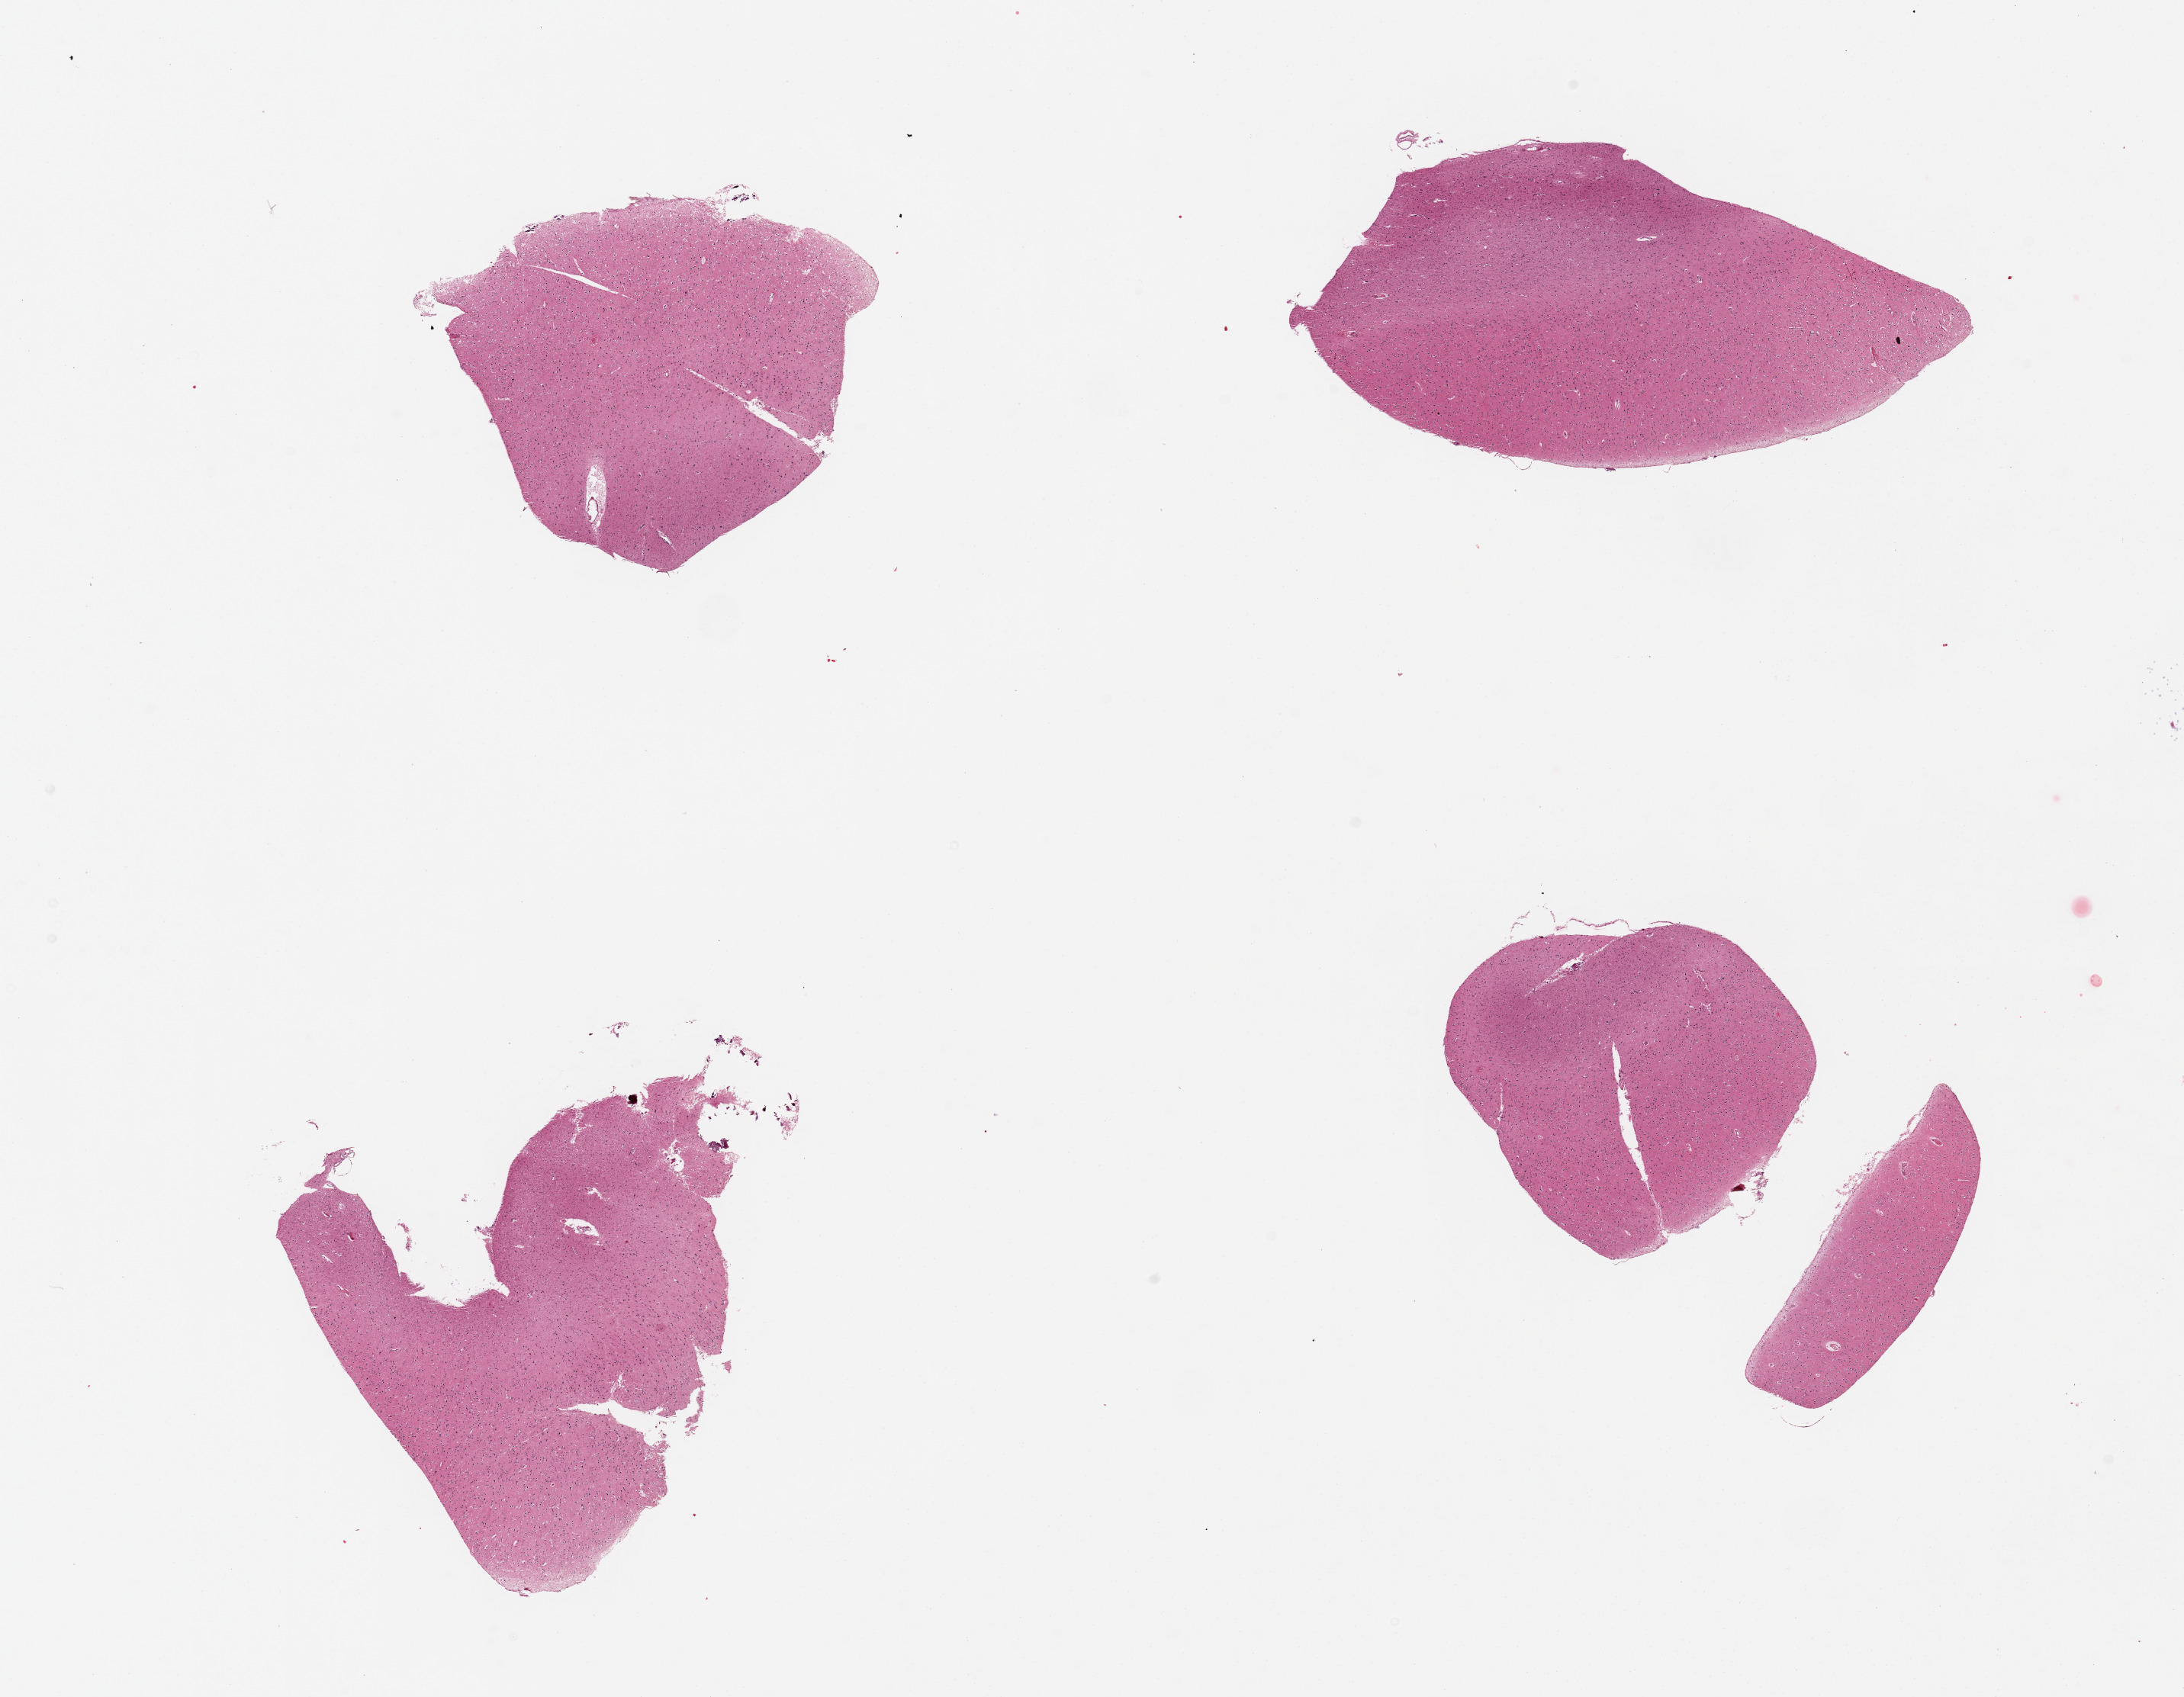
Digitized haematoxylin and eosin-stained section, a low-resolution overview of the entire scanned area, about 22.6 x 17.6 mm (slide scanned at 20x), PAXgene-fixed, paraffin-embedded tissue, section of cerebral cortex (target tissue), donor tissue sample. Donor sex: female.
Reviewer comment on this tissue sample: 4 pieces.